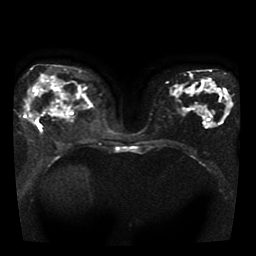
Breast MRI, one axial slice. Slice 20 of 41 in the series (ordered by position). Diffusion-weighted series; image 2 of 4 stored at this slice position (different b-values; order by instance number). 1.5 T. 256 × 256 image matrix. Female patient.
Structures marked on this image (expert manual segmentation):
- tumour on diffusion-weighted imaging: box from (x=28, y=112) to (x=41, y=121) px